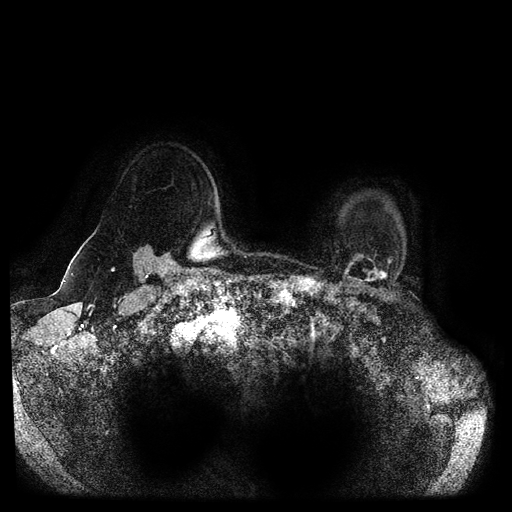
Breast MRI (dynamic contrast-enhanced, multi-phase), one axial slice. Position 87 of 116 along the scan axis. Dynamic contrast-enhanced series, time point 2 of 5 at this slice position (early post-contrast). 1.5 T. TE 2.6 ms, TR 5.3 ms. 2 mm slice thickness. 512 × 512 image matrix. Female patient, age 55 years.
Structures marked on this image (semi-automatic segmentation, software-assisted and operator-edited):
- breast lesion (labelled benign in the annotation): bounding box [x1, y1, x2, y2] px = [344, 254, 393, 286]